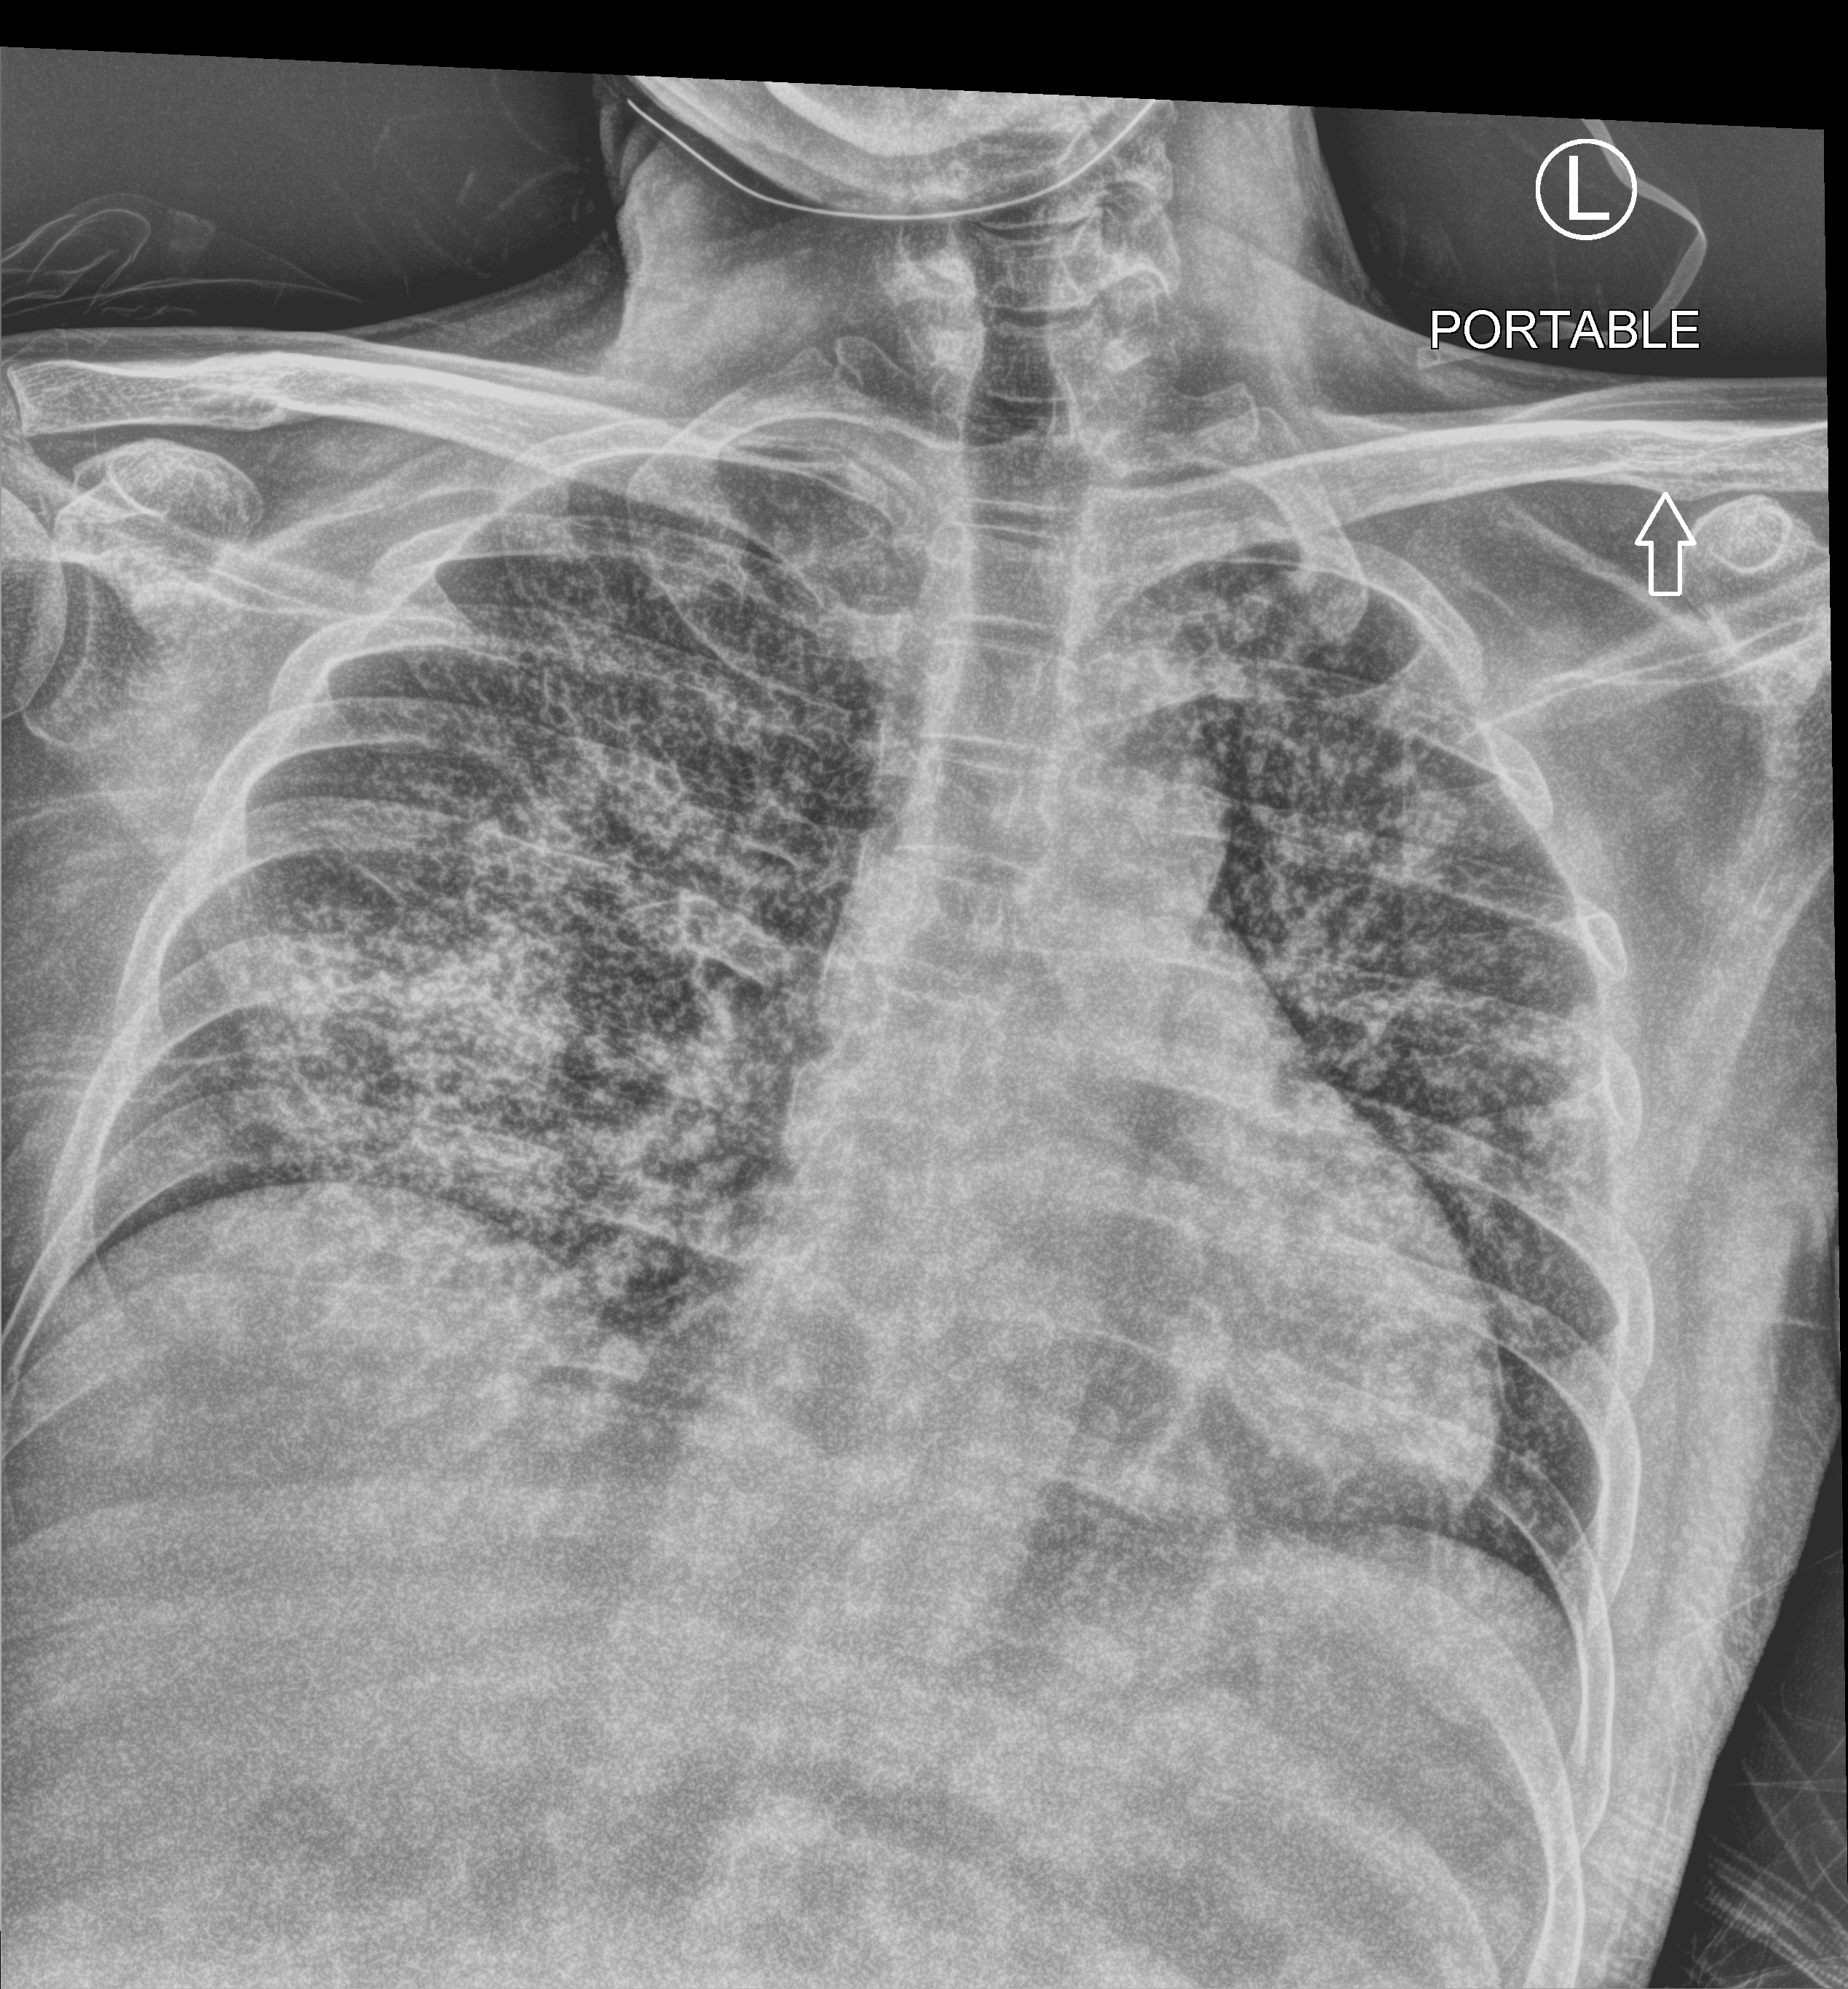
Bedside chest radiograph (computed radiography); anteroposterior (AP) projection. Male patient hospitalised with COVID-19, age 18–59 years.
From the hospital-stay record, not from the radiograph (when in the stay this image was taken is not recorded): diabetes (admission record): no; mechanically ventilated during this hospital stay: no.